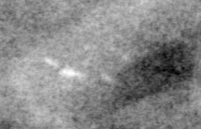
Crop from a digitized film mammogram around one marked abnormality, left breast, MLO view.
Finding: calcifications, morphology pleomorphic, distribution clustered; BI-RADS assessment category 4; subtlety rating 2 on a 1 (subtle) to 5 (obvious) scale; pathology (as recorded): benign.